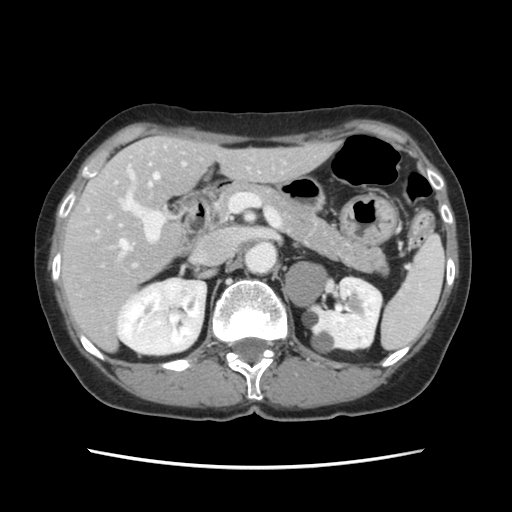
Contrast-enhanced abdominal CT, one axial slice; slice 70 of 120 in the series (ordered by position); intravenous contrast given; soft-tissue window (W 400 / L 40 HU); 2.5 mm slice thickness; 512 × 512 image matrix. Female patient, age 70 years. Case-level facts recorded for this patient, not image findings: diagnosis: colorectal cancer liver metastases, imaged before liver resection; multiple liver metastases: no; largest metastasis: 2.5 cm.
Annotated regions visible in this slice (manually delineated by an expert):
- hepatic veins: bounding box (x1, y1, x2, y2) in pixels: (119, 173, 159, 254)
- liver: (62, 137, 335, 348)
- planned liver remnant (the part of the liver to remain after resection): (87, 137, 334, 278)
- portal vein (with intrahepatic branches): (108, 146, 231, 267)